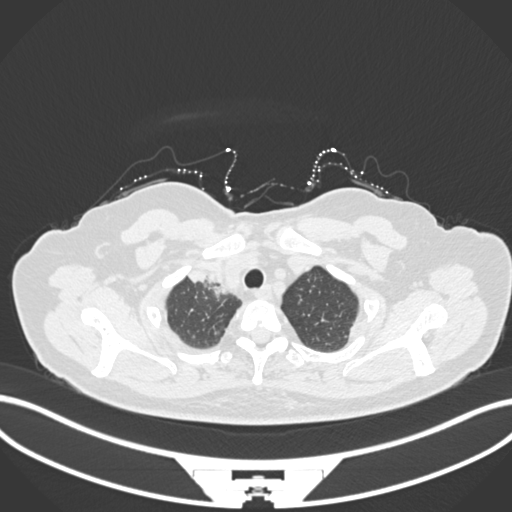
Chest CT, one axial slice. Position 150 of 172 along the scan axis. Reconstruction kernel B30f. Lung window (W 1500 / L -600 HU). 1 mm slice thickness. 512 × 512 image matrix. Female patient, age 52 years. Case-level facts recorded for this patient, not image findings: clinical TNM (as recorded): T3 N1 M1.
Structures marked on this image (rectangle marked by the reading radiologist):
- lung tumour (recorded histology: adenocarcinoma): bounding box (x1, y1, x2, y2) in pixels: (187, 263, 230, 298)